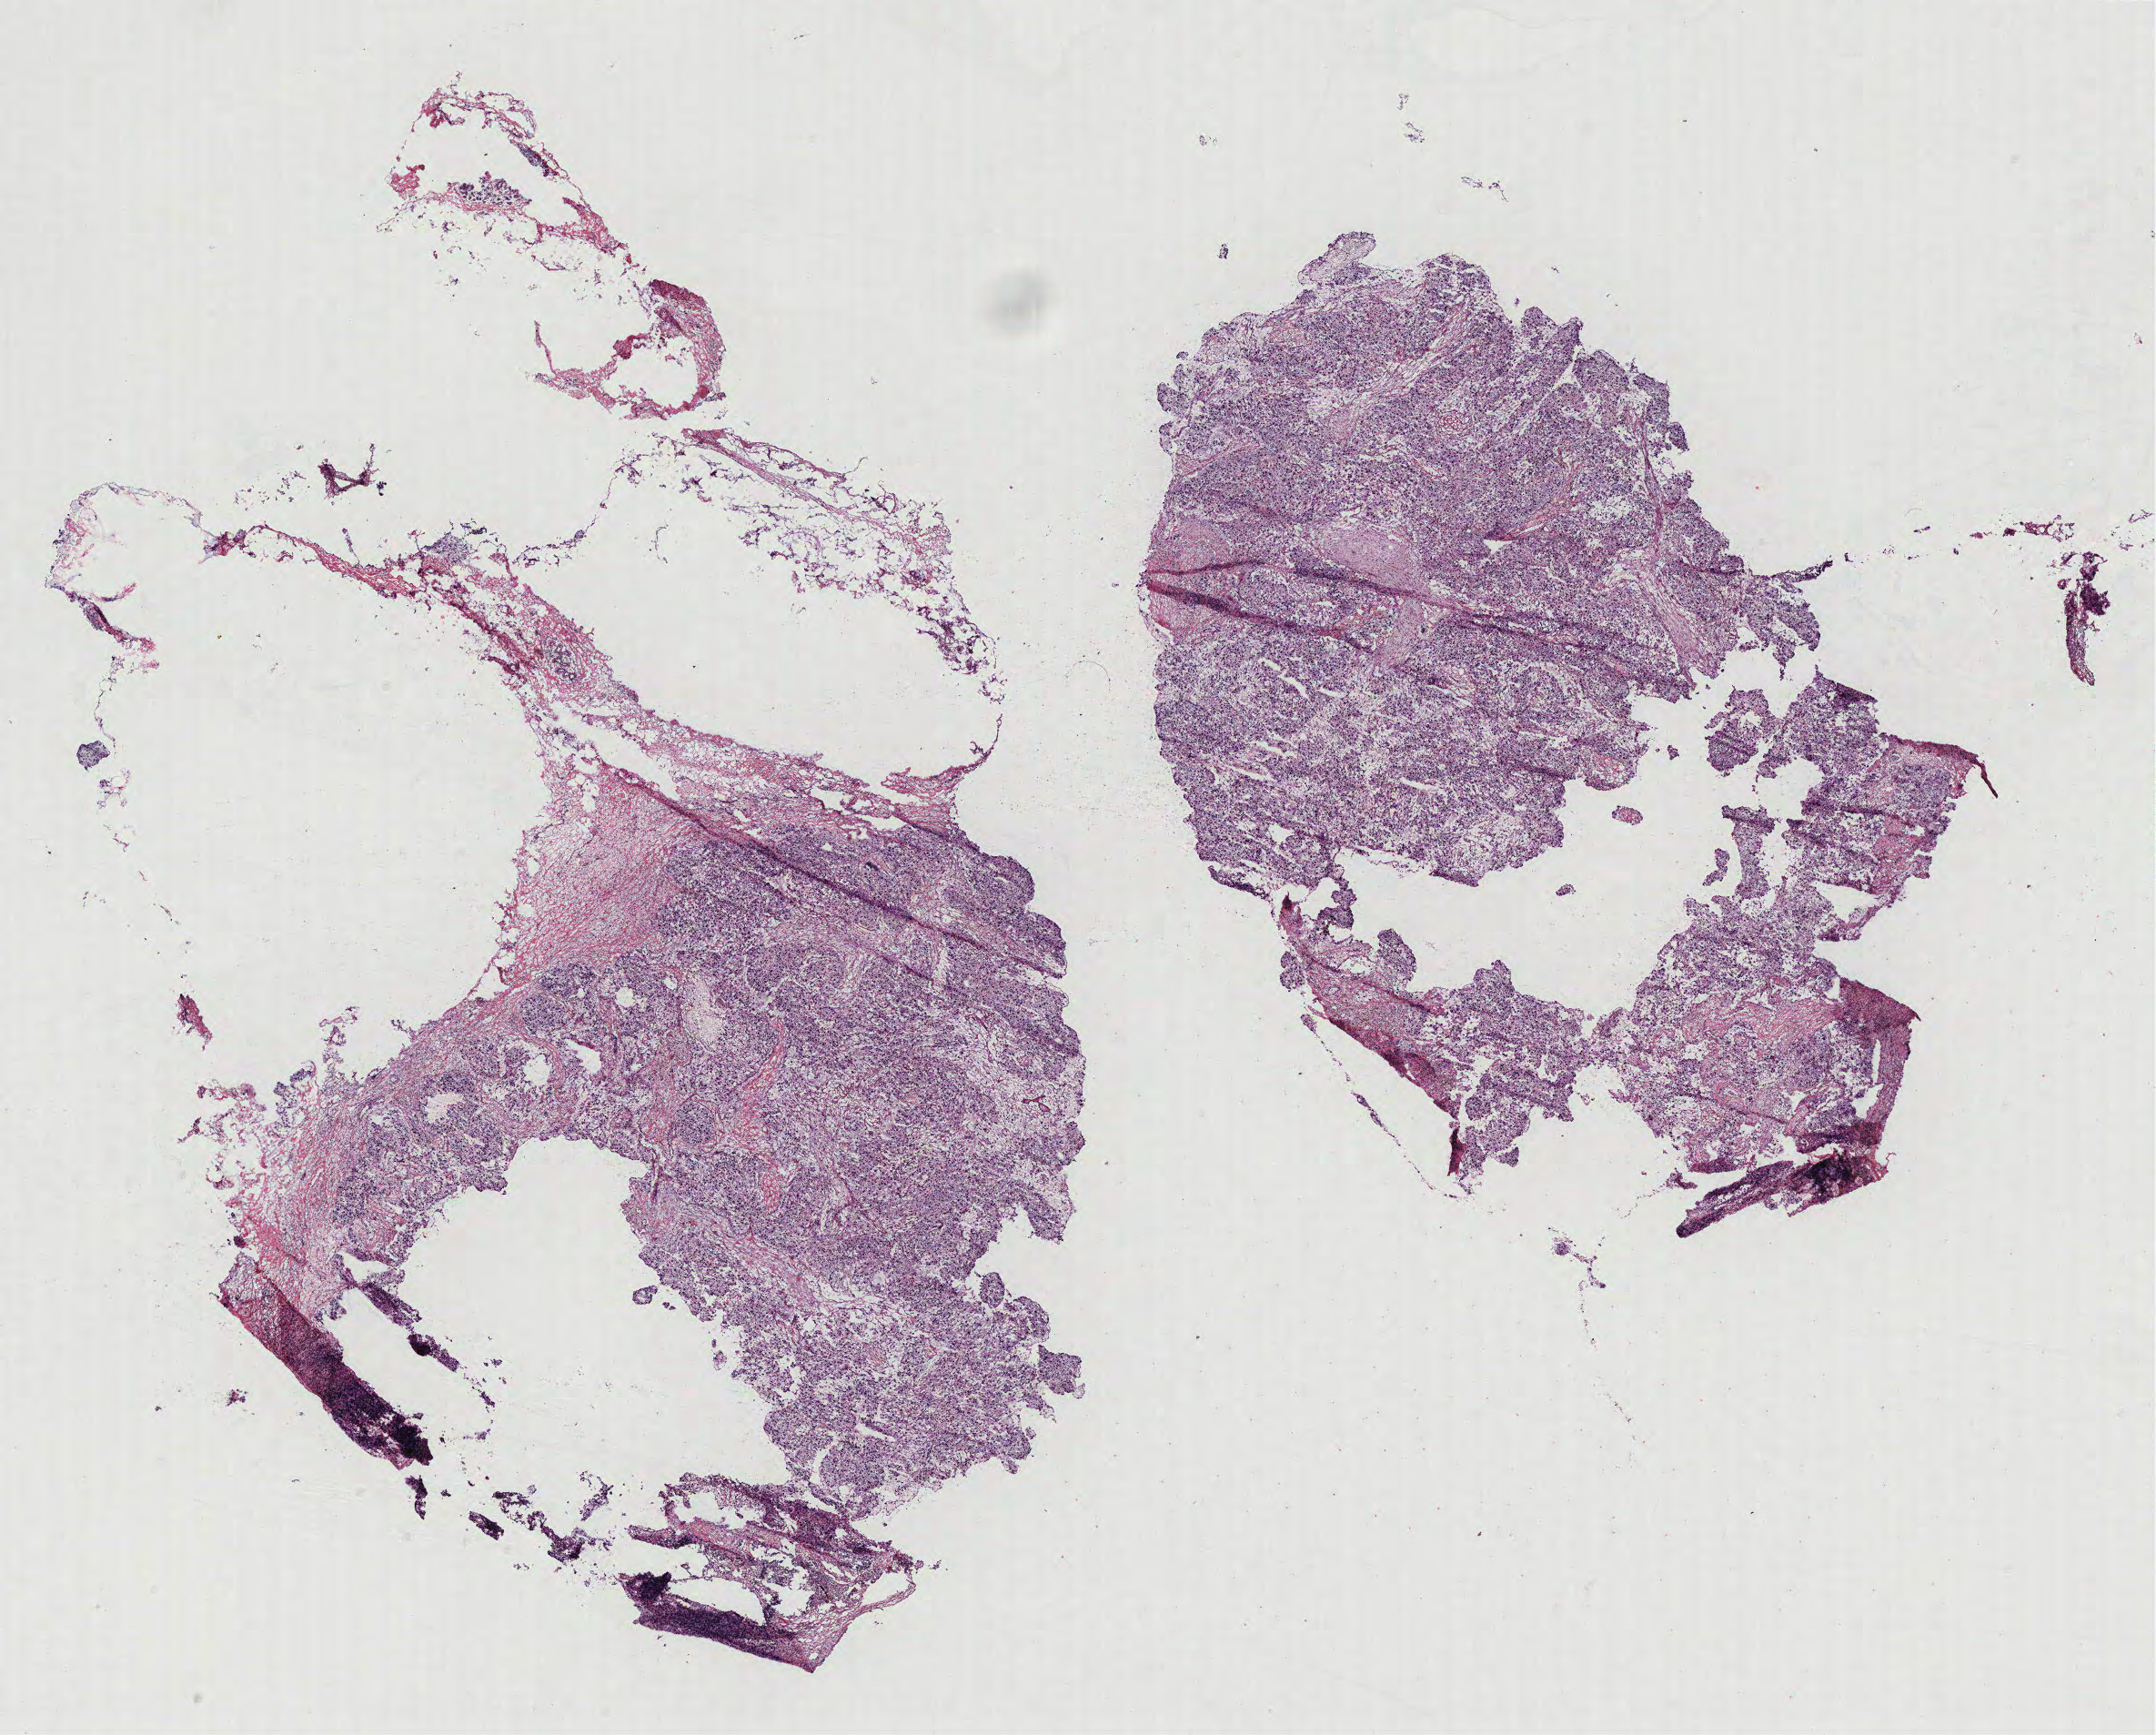
Digitized Hematoxylin and eosin (H&E) stained tissue section (whole slide) — shown as a low-resolution overview of the whole scanned area (about 19.0 x 15.3 mm, from a 40x scan); breast, tissue type not recorded.
* patient diagnosis (cohort enrolment): breast cancer (breast)